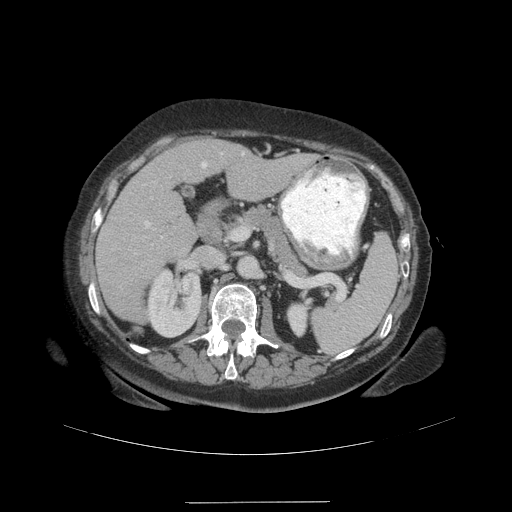
Contrast-enhanced abdominal CT (liver protocol), one axial slice; slice 57 of 99 in the series (ordered by position); reconstruction kernel STANDARD; 140 kVp; soft-tissue window (W 400 / L 40 HU); 512 × 512 image matrix. From the clinical record (not read from this slice): diagnosis: hepatocellular carcinoma (patient treated with transarterial chemoembolisation; whether this scan precedes or follows treatment is not stated here); TNM stage (as recorded): Stage-IVA; Child-Pugh class: A; tumour nodularity: multinodular.
Annotated regions visible in this slice (semi-automatic segmentation, software-assisted and operator-edited):
- liver parenchyma outside the tumour (the mass and vessels are separate outlines, so this box may not span the whole liver): box from (x=96, y=140) to (x=312, y=320) px
- liver vessels: (x=144, y=152)–(x=245, y=238)